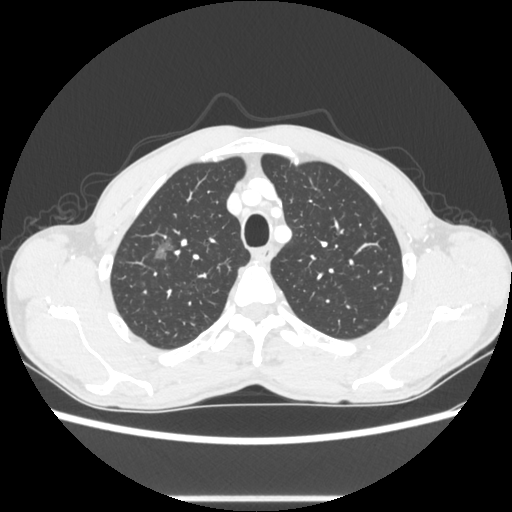
Chest CT, one axial slice; slice 228 of 289 in the series (ordered by position); reconstruction kernel STANDARD; lung window (W 1500 / L -600 HU); 1.25 mm slice thickness; 512 × 512 image matrix, field of view 350 × 350 mm. Patient: male, 54 years. Case-level facts recorded for this patient, not image findings: clinical TNM (as recorded): T1a N0 M0.
Structures marked on this image (rectangle marked by the reading radiologist):
- lung tumour (recorded histology: adenocarcinoma): box from (x=149, y=230) to (x=180, y=271) px